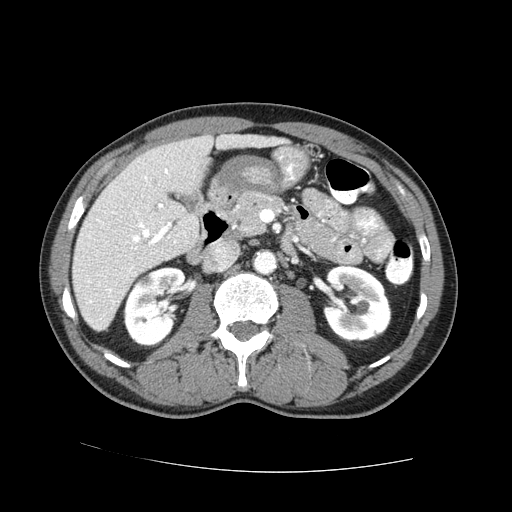
Contrast-enhanced abdominal CT (liver protocol), one axial slice; slice 29 of 73 in the series (ordered by position); reconstruction kernel STANDARD; 100 kVp; one of 2 acquisitions stored at this slice position; soft-tissue window (W 400 / L 40 HU); 2.5 mm slice thickness; 512 × 512 image matrix, field of view 380 × 380 mm. From the clinical record (not read from this slice): diagnosis: hepatocellular carcinoma (patient treated with transarterial chemoembolisation; whether this scan precedes or follows treatment is not stated here); TNM stage (as recorded): Stage-IVA; Child-Pugh class: A.
Structures marked on this image (semi-automatically segmented with operator editing):
- liver parenchyma outside the tumour (the mass and vessels are separate outlines, so this box may not span the whole liver): box from (x=72, y=134) to (x=278, y=330) px
- liver vessels: (x=89, y=169)–(x=171, y=302)